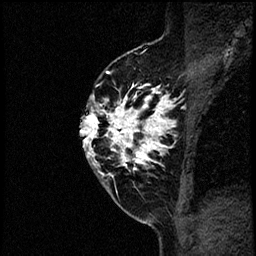
Breast MRI (dynamic contrast-enhanced), one sagittal slice; position 41 of 60 along the scan axis; dynamic contrast-enhanced study with each time point stored as its own series, time point 2 of 4 at this slice position (early post-contrast, ordered by acquisition time); 1.5 T; TE 4.2 ms, TR 17.6 ms; 2 mm slice thickness; 256 × 256 image matrix, field of view 200 × 200 mm. Female patient, age 40 years. Case-level facts recorded for this patient, not image findings: setting: breast cancer imaged before/during neoadjuvant chemotherapy; receptor status: HER2-positive.
Structures marked on this image (semi-automatically segmented with operator editing):
- analysis volume of interest (the breast-tissue region the enhancement analysis was run in; not a lesion): bounding box <81,56,197,205> (left, top, right, bottom; pixels)
- tumour enhancement mask (voxels above the 100 % enhancement threshold inside the analysis volume of interest): <81,71,178,177>